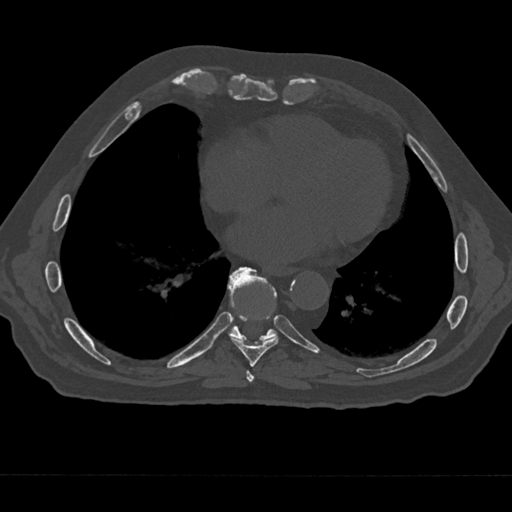
CT including the spine, one axial slice; slice 295 of 797 in the series (ordered by position); reconstruction kernel Br40s/3; 120 kVp; bone window (W 1800 / L 400 HU); 0.5 mm slice thickness; 512 × 512 image matrix, field of view 377 × 377 mm. Patient: male, 75 years. Case-level facts recorded for this patient, not image findings: primary cancer: renal; vertebrae with lytic lesions (as recorded): T4.
Structures marked on this image (semi-automatic segmentation, software-assisted and operator-edited):
- T7 vertebra: bounding box (x1, y1, x2, y2) in pixels: (244, 370, 258, 385)
- T8 vertebra: (230, 282, 279, 367)
- T9 vertebra: (227, 267, 277, 341)